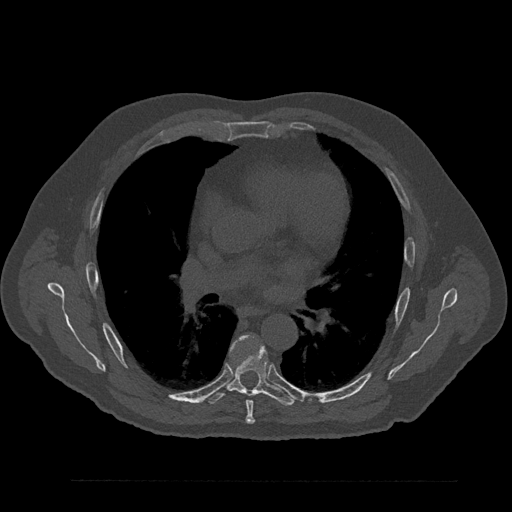
CT including the spine, one axial slice. Position 526 of 797 along the scan axis. Reconstruction kernel Br40s/3. 120 kVp. Bone window (W 1800 / L 400 HU). 0.5 mm slice thickness. 512 × 512 image matrix, field of view 430 × 430 mm. Male patient, age 61 years. Case-level facts recorded for this patient, not image findings: primary cancer: prostate.
Structures marked on this image (semi-automatically segmented with operator editing):
- T6 vertebra: bounding box <231,336,255,424> (left, top, right, bottom; pixels)
- T7 vertebra: <205,344,295,406>